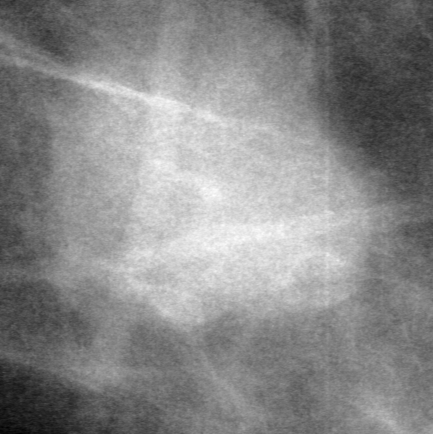
Crop from a digitized film mammogram around one marked abnormality, left breast, CC view, BI-RADS breast density category 1 (scale 1–4).
- Mass, shape lobulated, margins circumscribed; BI-RADS assessment category 0; pathology (as recorded): benign.